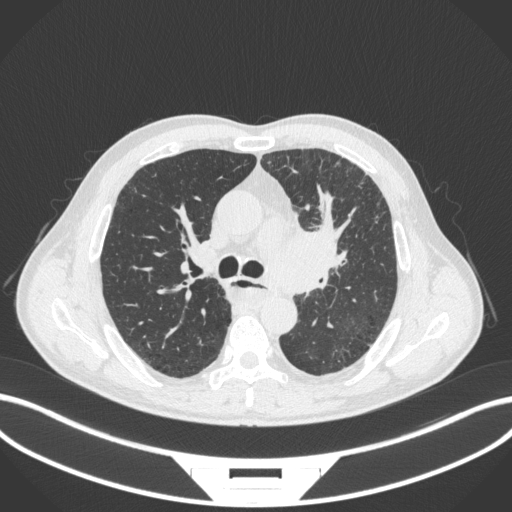
Chest CT, one axial slice. Position 246 of 411 along the scan axis. 120 kVp. Lung window (W 1500 / L -600 HU). 1 mm slice thickness. 512 × 512 image matrix, field of view 400 × 400 mm. Male patient, age 57 years. Case-level facts recorded for this patient, not image findings: clinical TNM (as recorded): T2a N1 M0.
Structures marked on this image (rectangle marked by the reading radiologist):
- lung tumour (recorded histology: squamous cell carcinoma): bounding box [x1, y1, x2, y2] px = [265, 218, 343, 291]